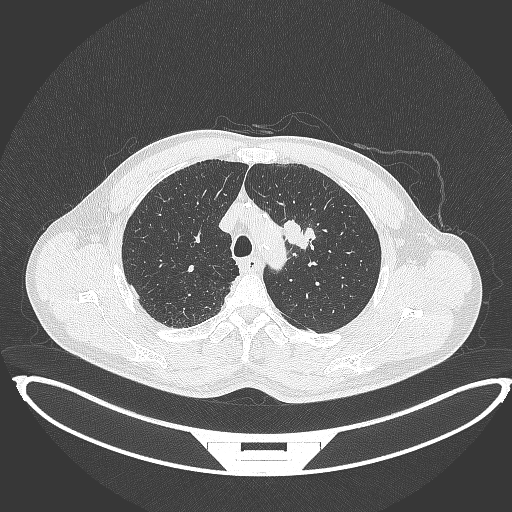
Chest CT, one axial slice. Slice 336 of 395 in the series (ordered by position). Lung window (W 1500 / L -600 HU). 1 mm slice thickness. 512 × 512 image matrix, field of view 457 × 457 mm. Patient: male, 60 years. Case-level facts recorded for this patient, not image findings: clinical TNM (as recorded): T2a N0 M0.
Annotated regions visible in this slice (bounding box drawn by a radiologist):
- lung tumour (recorded histology: squamous cell carcinoma): bounding box (x1, y1, x2, y2) in pixels: (282, 215, 317, 251)